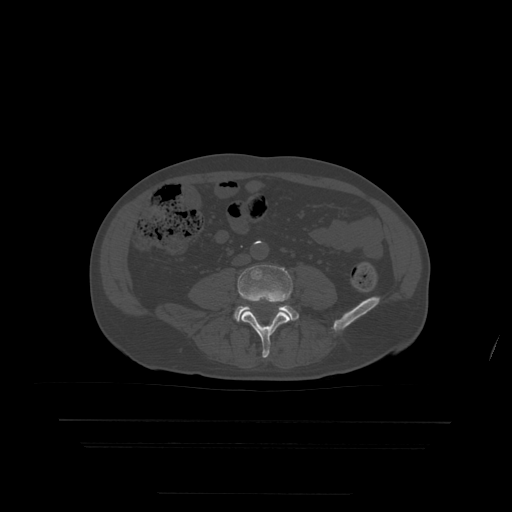
CT including the spine, one axial slice. Slice 89 of 522 in the series (ordered by position). Bone window (W 1800 / L 400 HU). 512 × 512 image matrix. Patient age 68 years. From the clinical record (not read from this slice): primary cancer: urothelial.
Outlined on this slice (semi-automatically segmented with operator editing):
- L4 vertebra: bounding box <238,265,293,358> (left, top, right, bottom; pixels)
- L5 vertebra: <235,306,299,322>